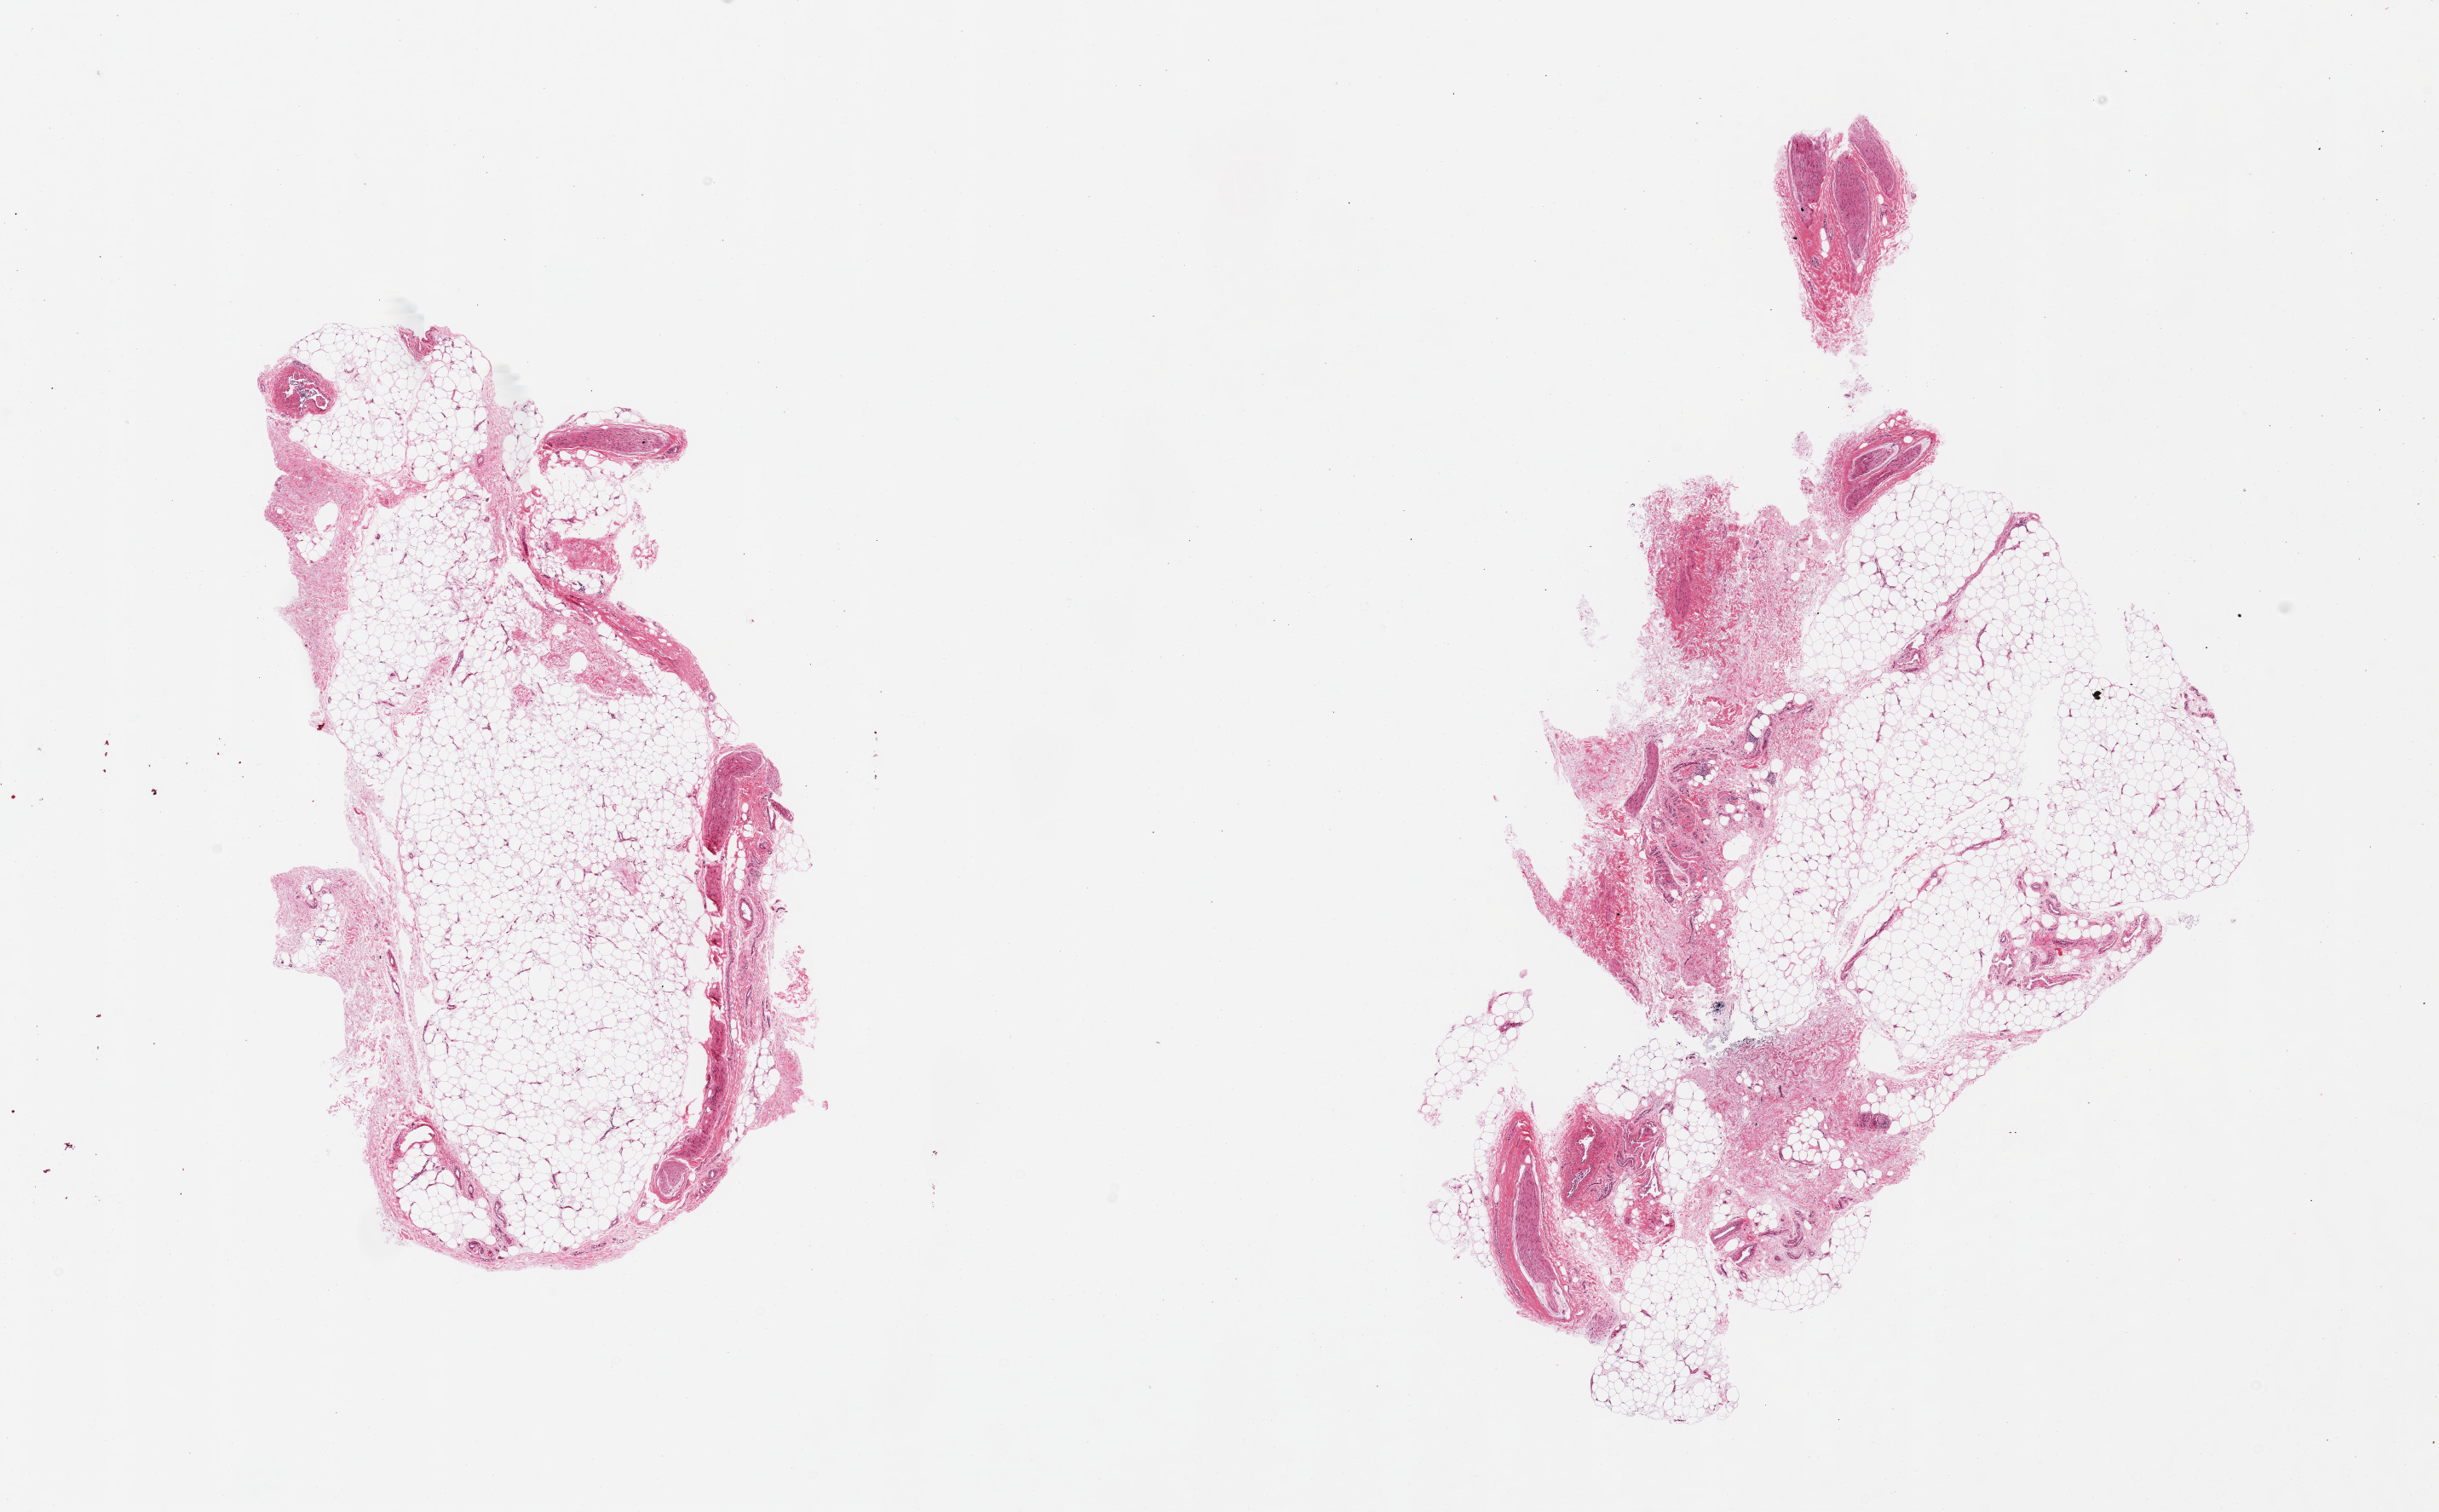
Hematoxylin and eosin (H&E) whole-slide image, brightfield, low-resolution overview of the scanned area, about 22.6 x 14.0 mm (slide scanned at 20x), PAXgene-fixed paraffin-embedded (PFPE) section, section of adipose tissue (target tissue), donor tissue sample.
Review note (as recorded): 2 pieces, ~30-40% peripheral nerve, fascia, and vascular elements.